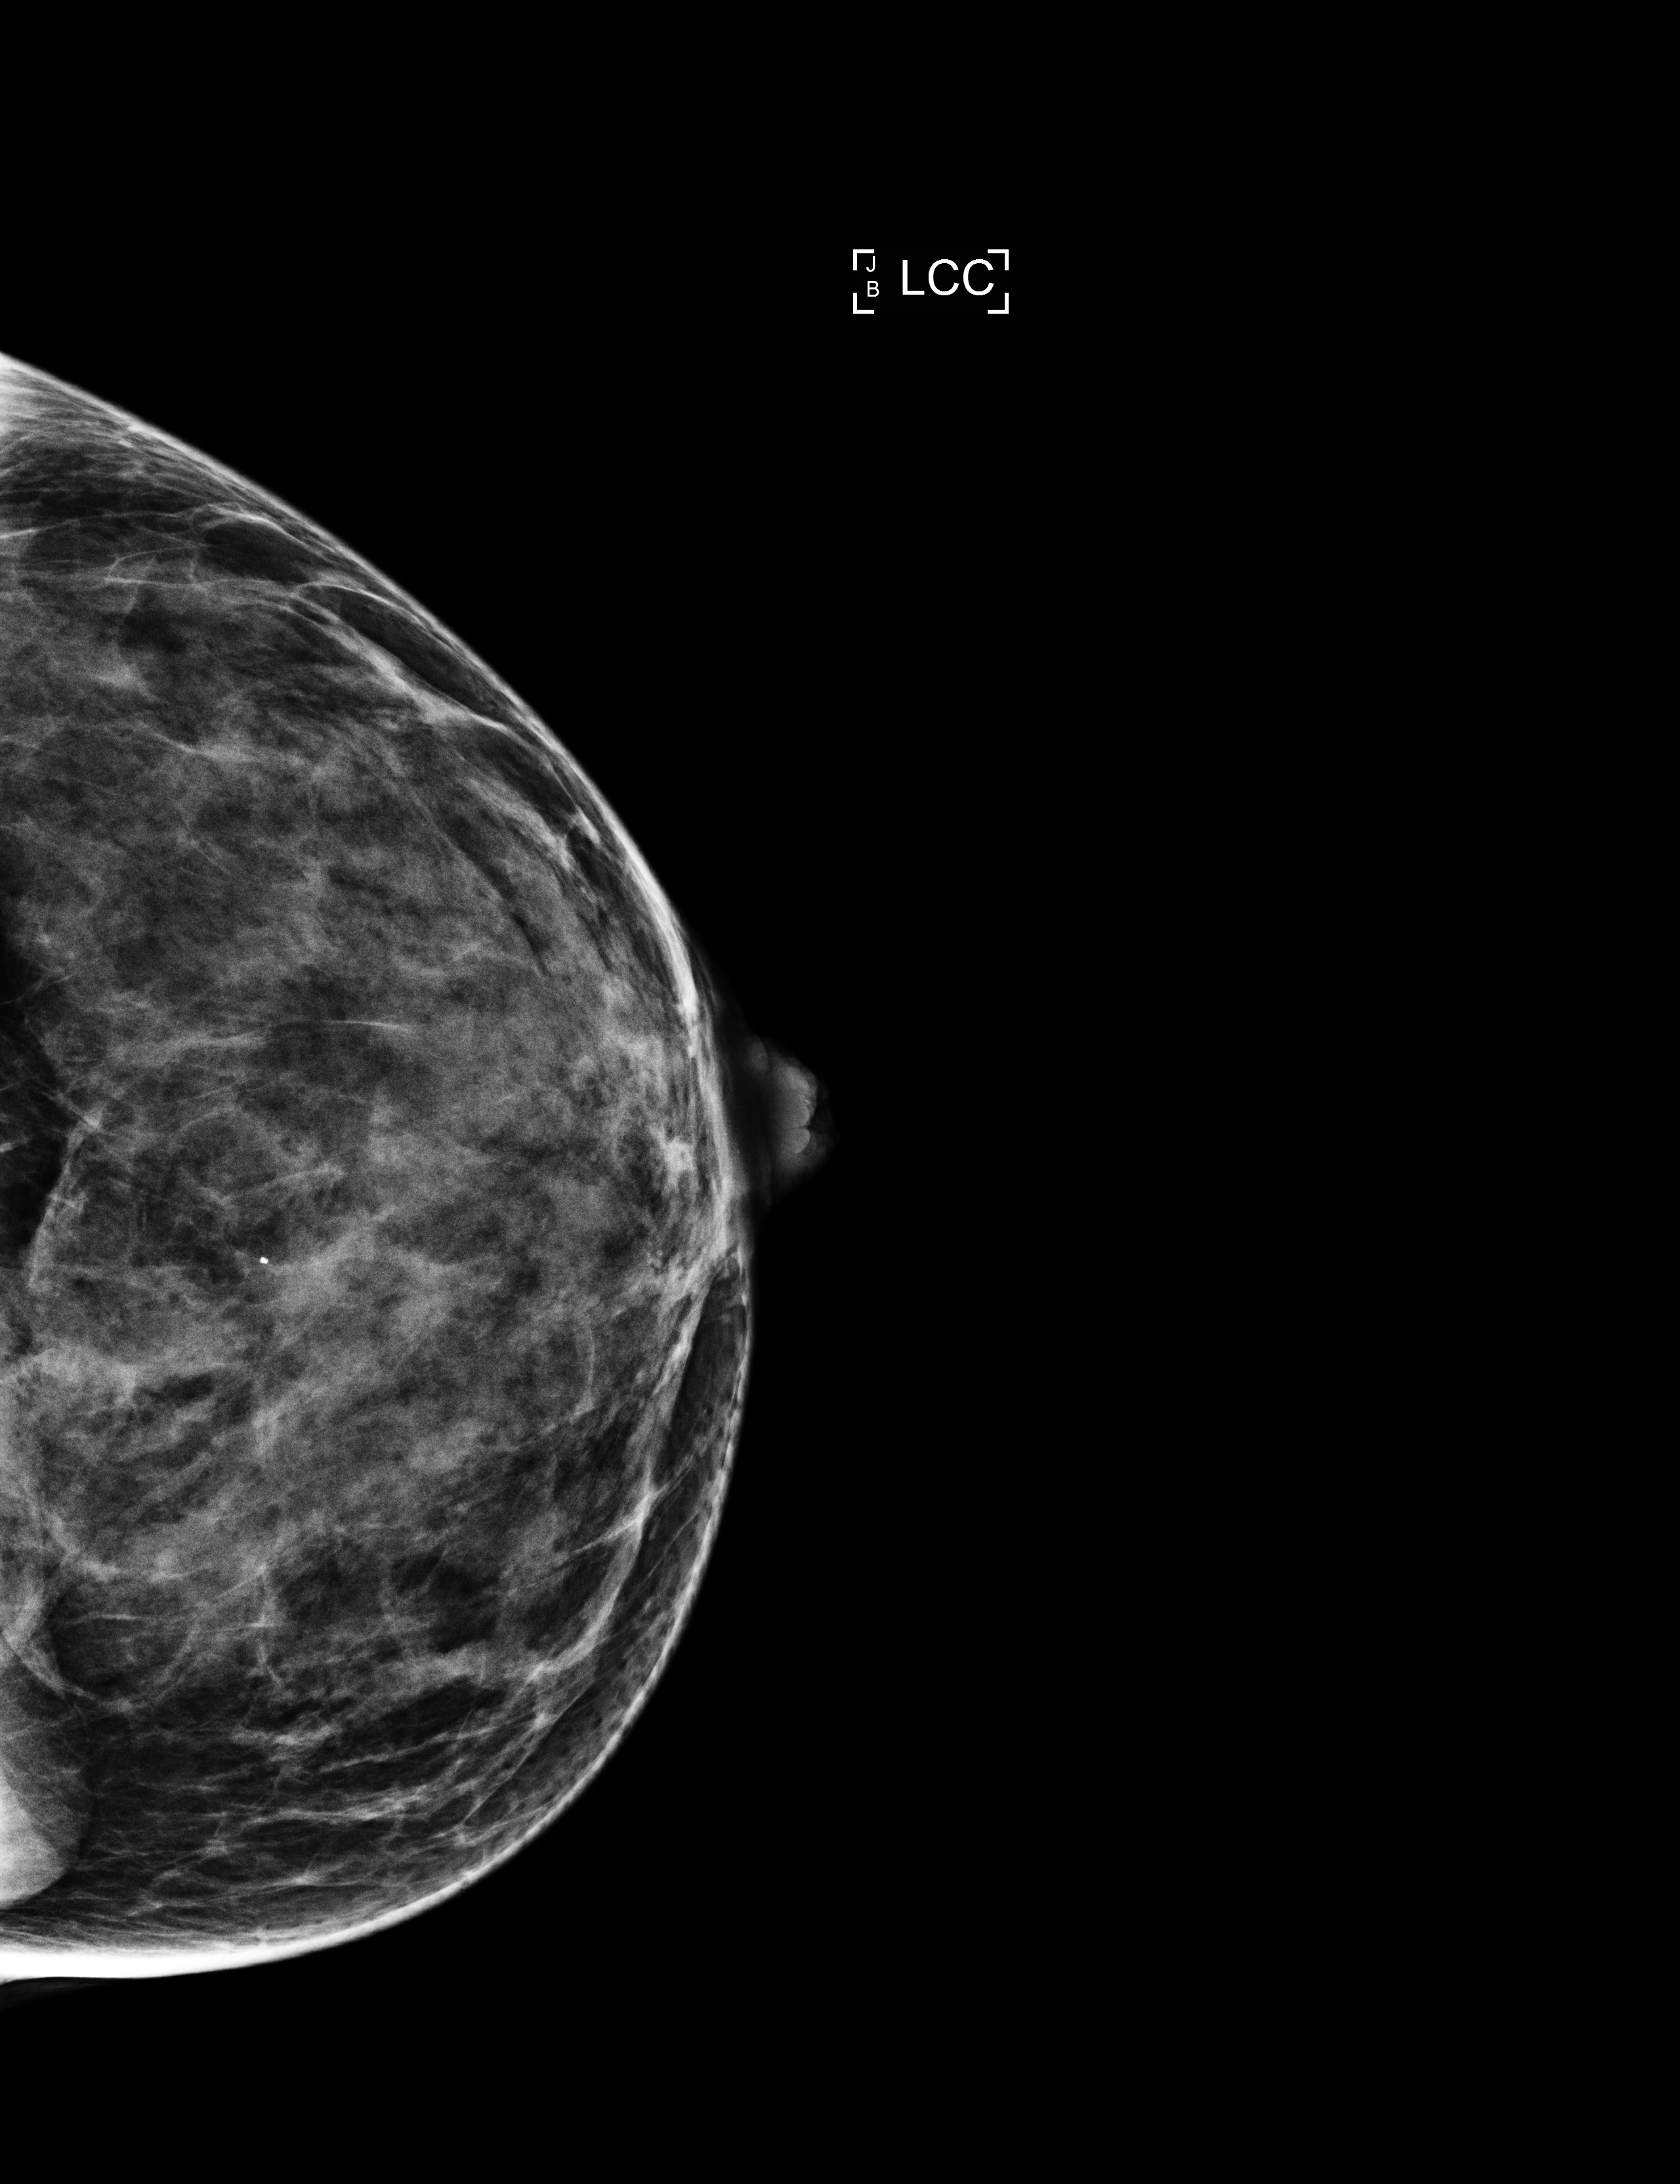
Screening examination. Patient aged 47 years (female).
Image type: full-field digital mammogram. Breast: left. Projection: CC view.